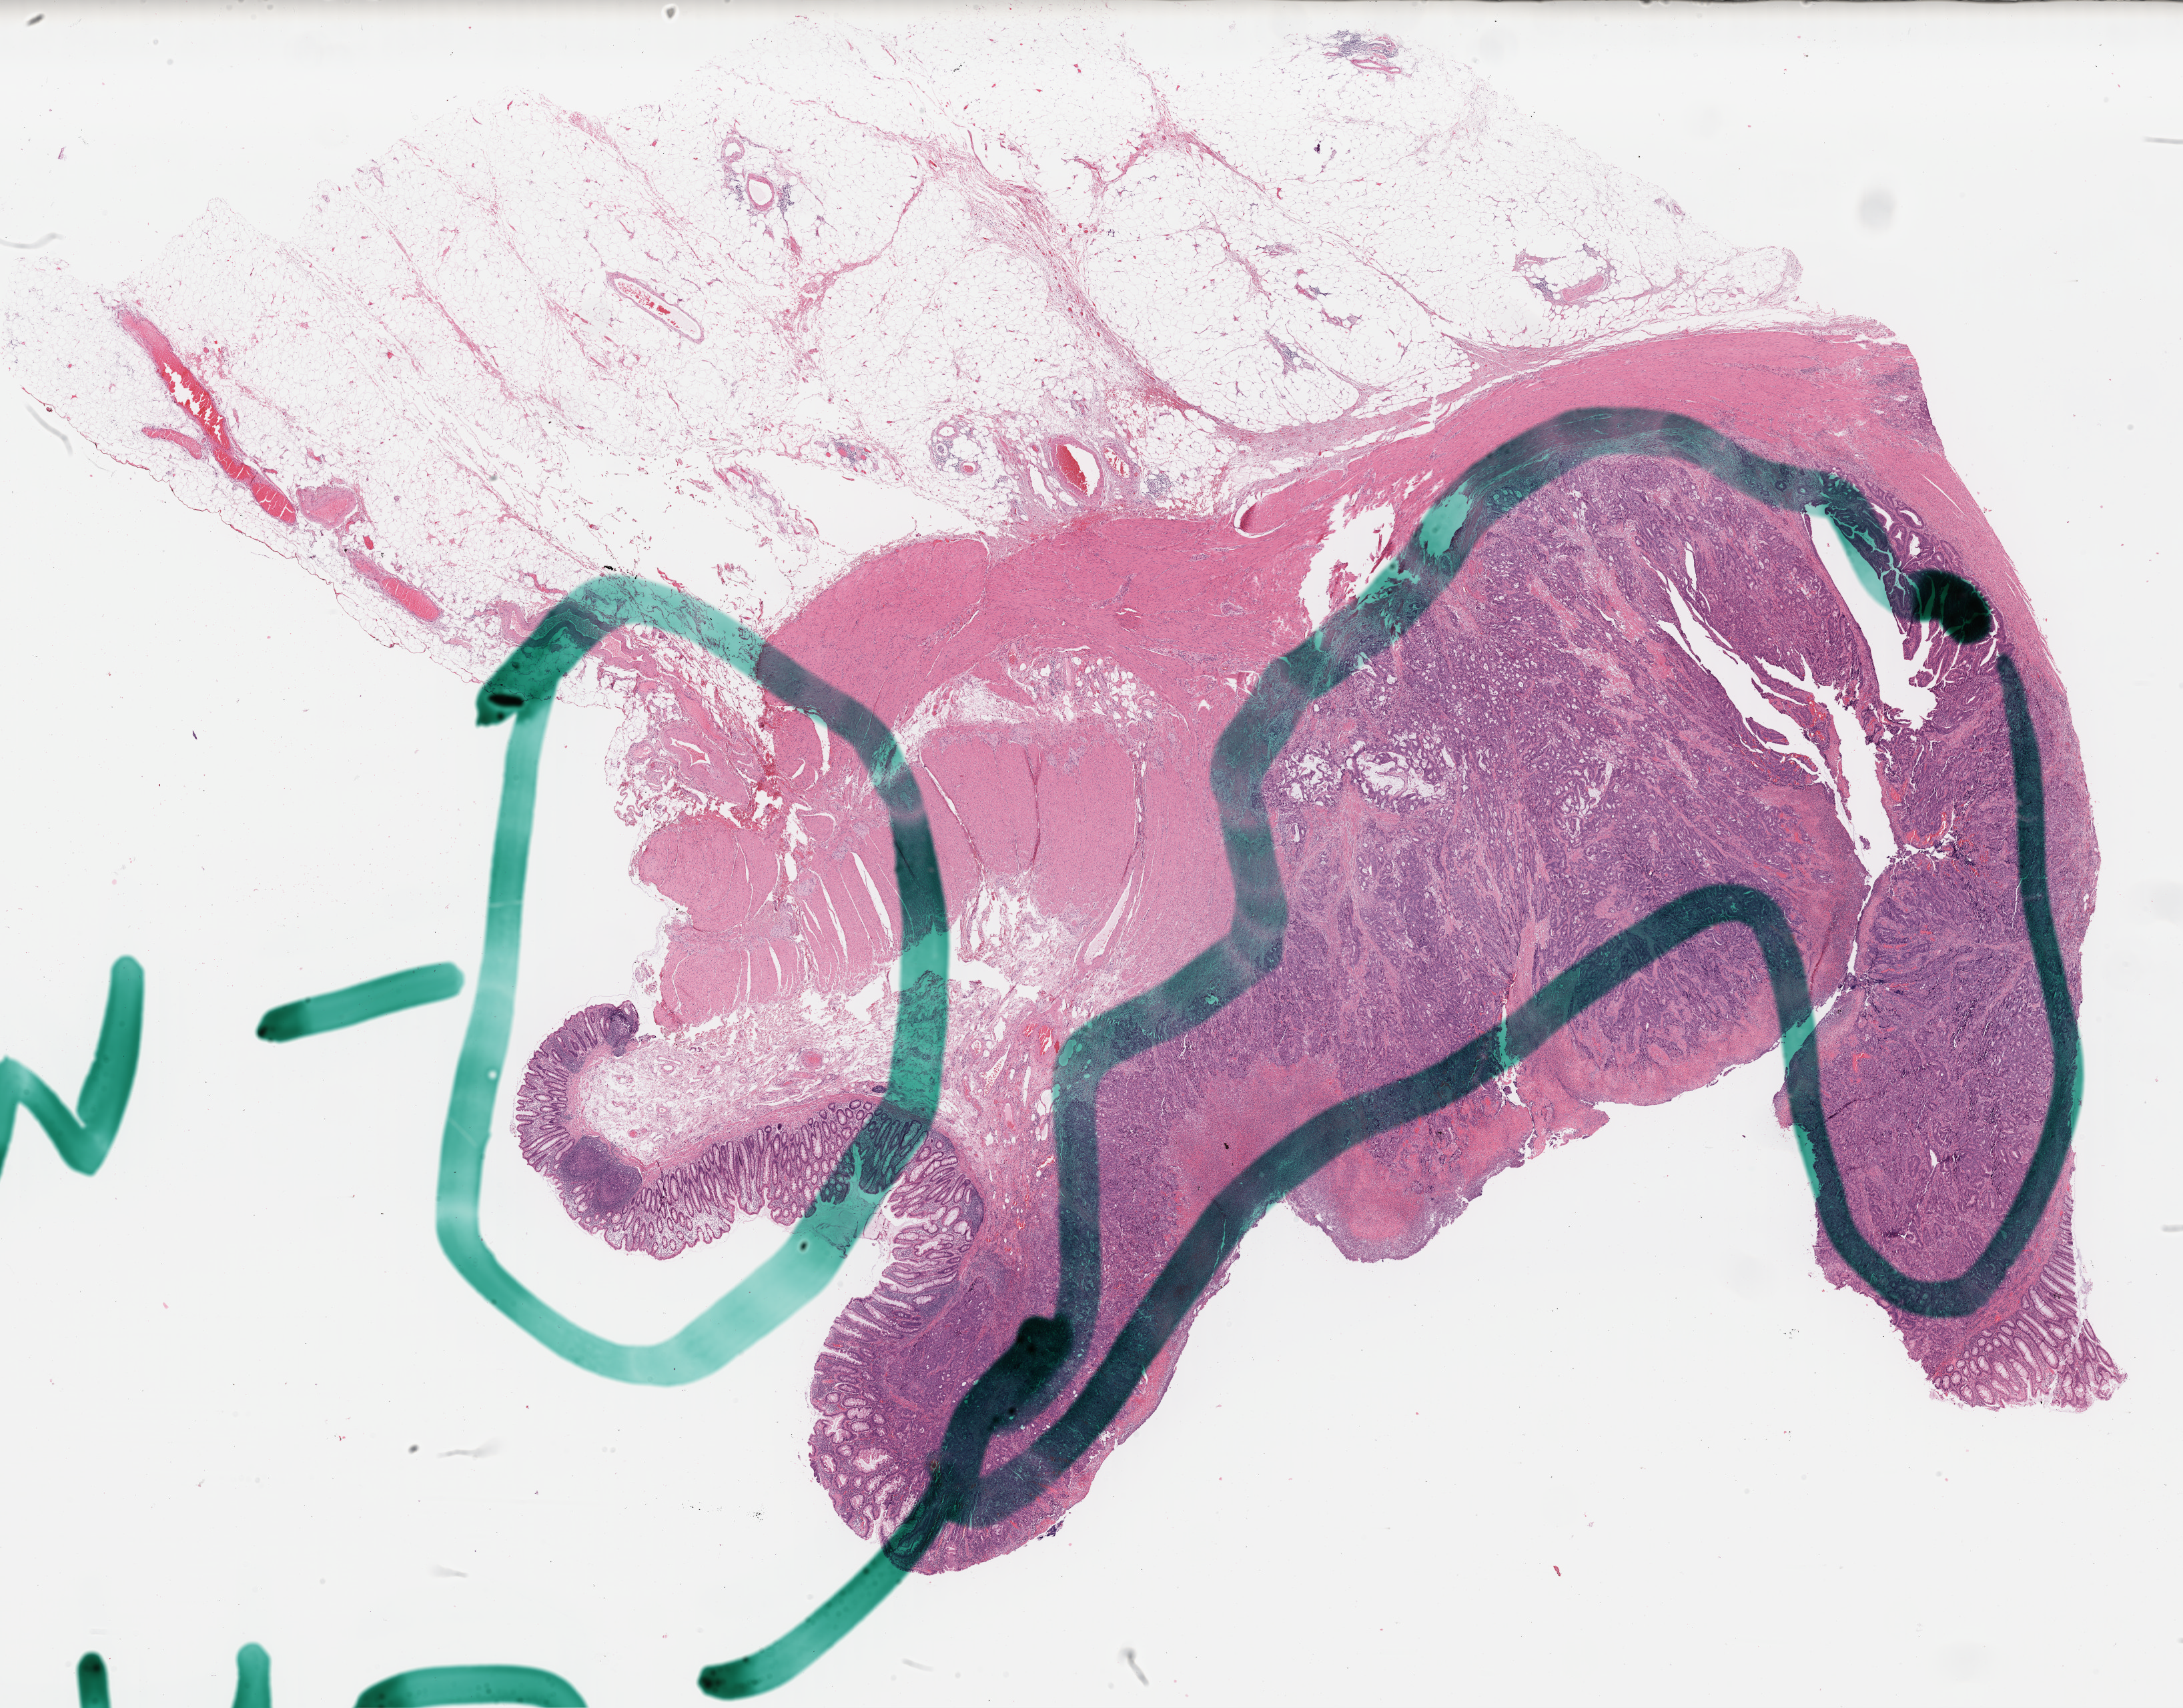
Hematoxylin and eosin (H&E) stained whole-slide image, a low-resolution overview of the entire scanned area, about 25.8 x 20.2 mm (acquisition: 40x scan), FFPE section, rectum, primary tumour sample. Patient: female, age at initial diagnosis 72 years.
Diagnosis: Adenocarcinoma, NOS. AJCC pathologic stage: IIA. Lymph nodes positive (case pathology): 0 of 16 examined.